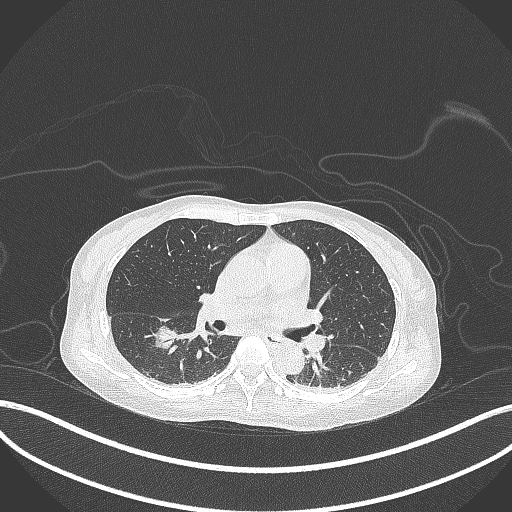
Chest CT, one axial slice; position 169 of 261 along the scan axis; reconstruction kernel B70f; 120 kVp; lung window (W 1500 / L -600 HU); 512 × 512 image matrix, field of view 400 × 400 mm. Patient: female, 44 years. From the clinical record (not read from this slice): clinical TNM (as recorded): T1c N0 M0.
Outlined on this slice (rectangle marked by the reading radiologist):
- lung tumour (recorded histology: adenocarcinoma): bounding box <151,321,182,353> (left, top, right, bottom; pixels)